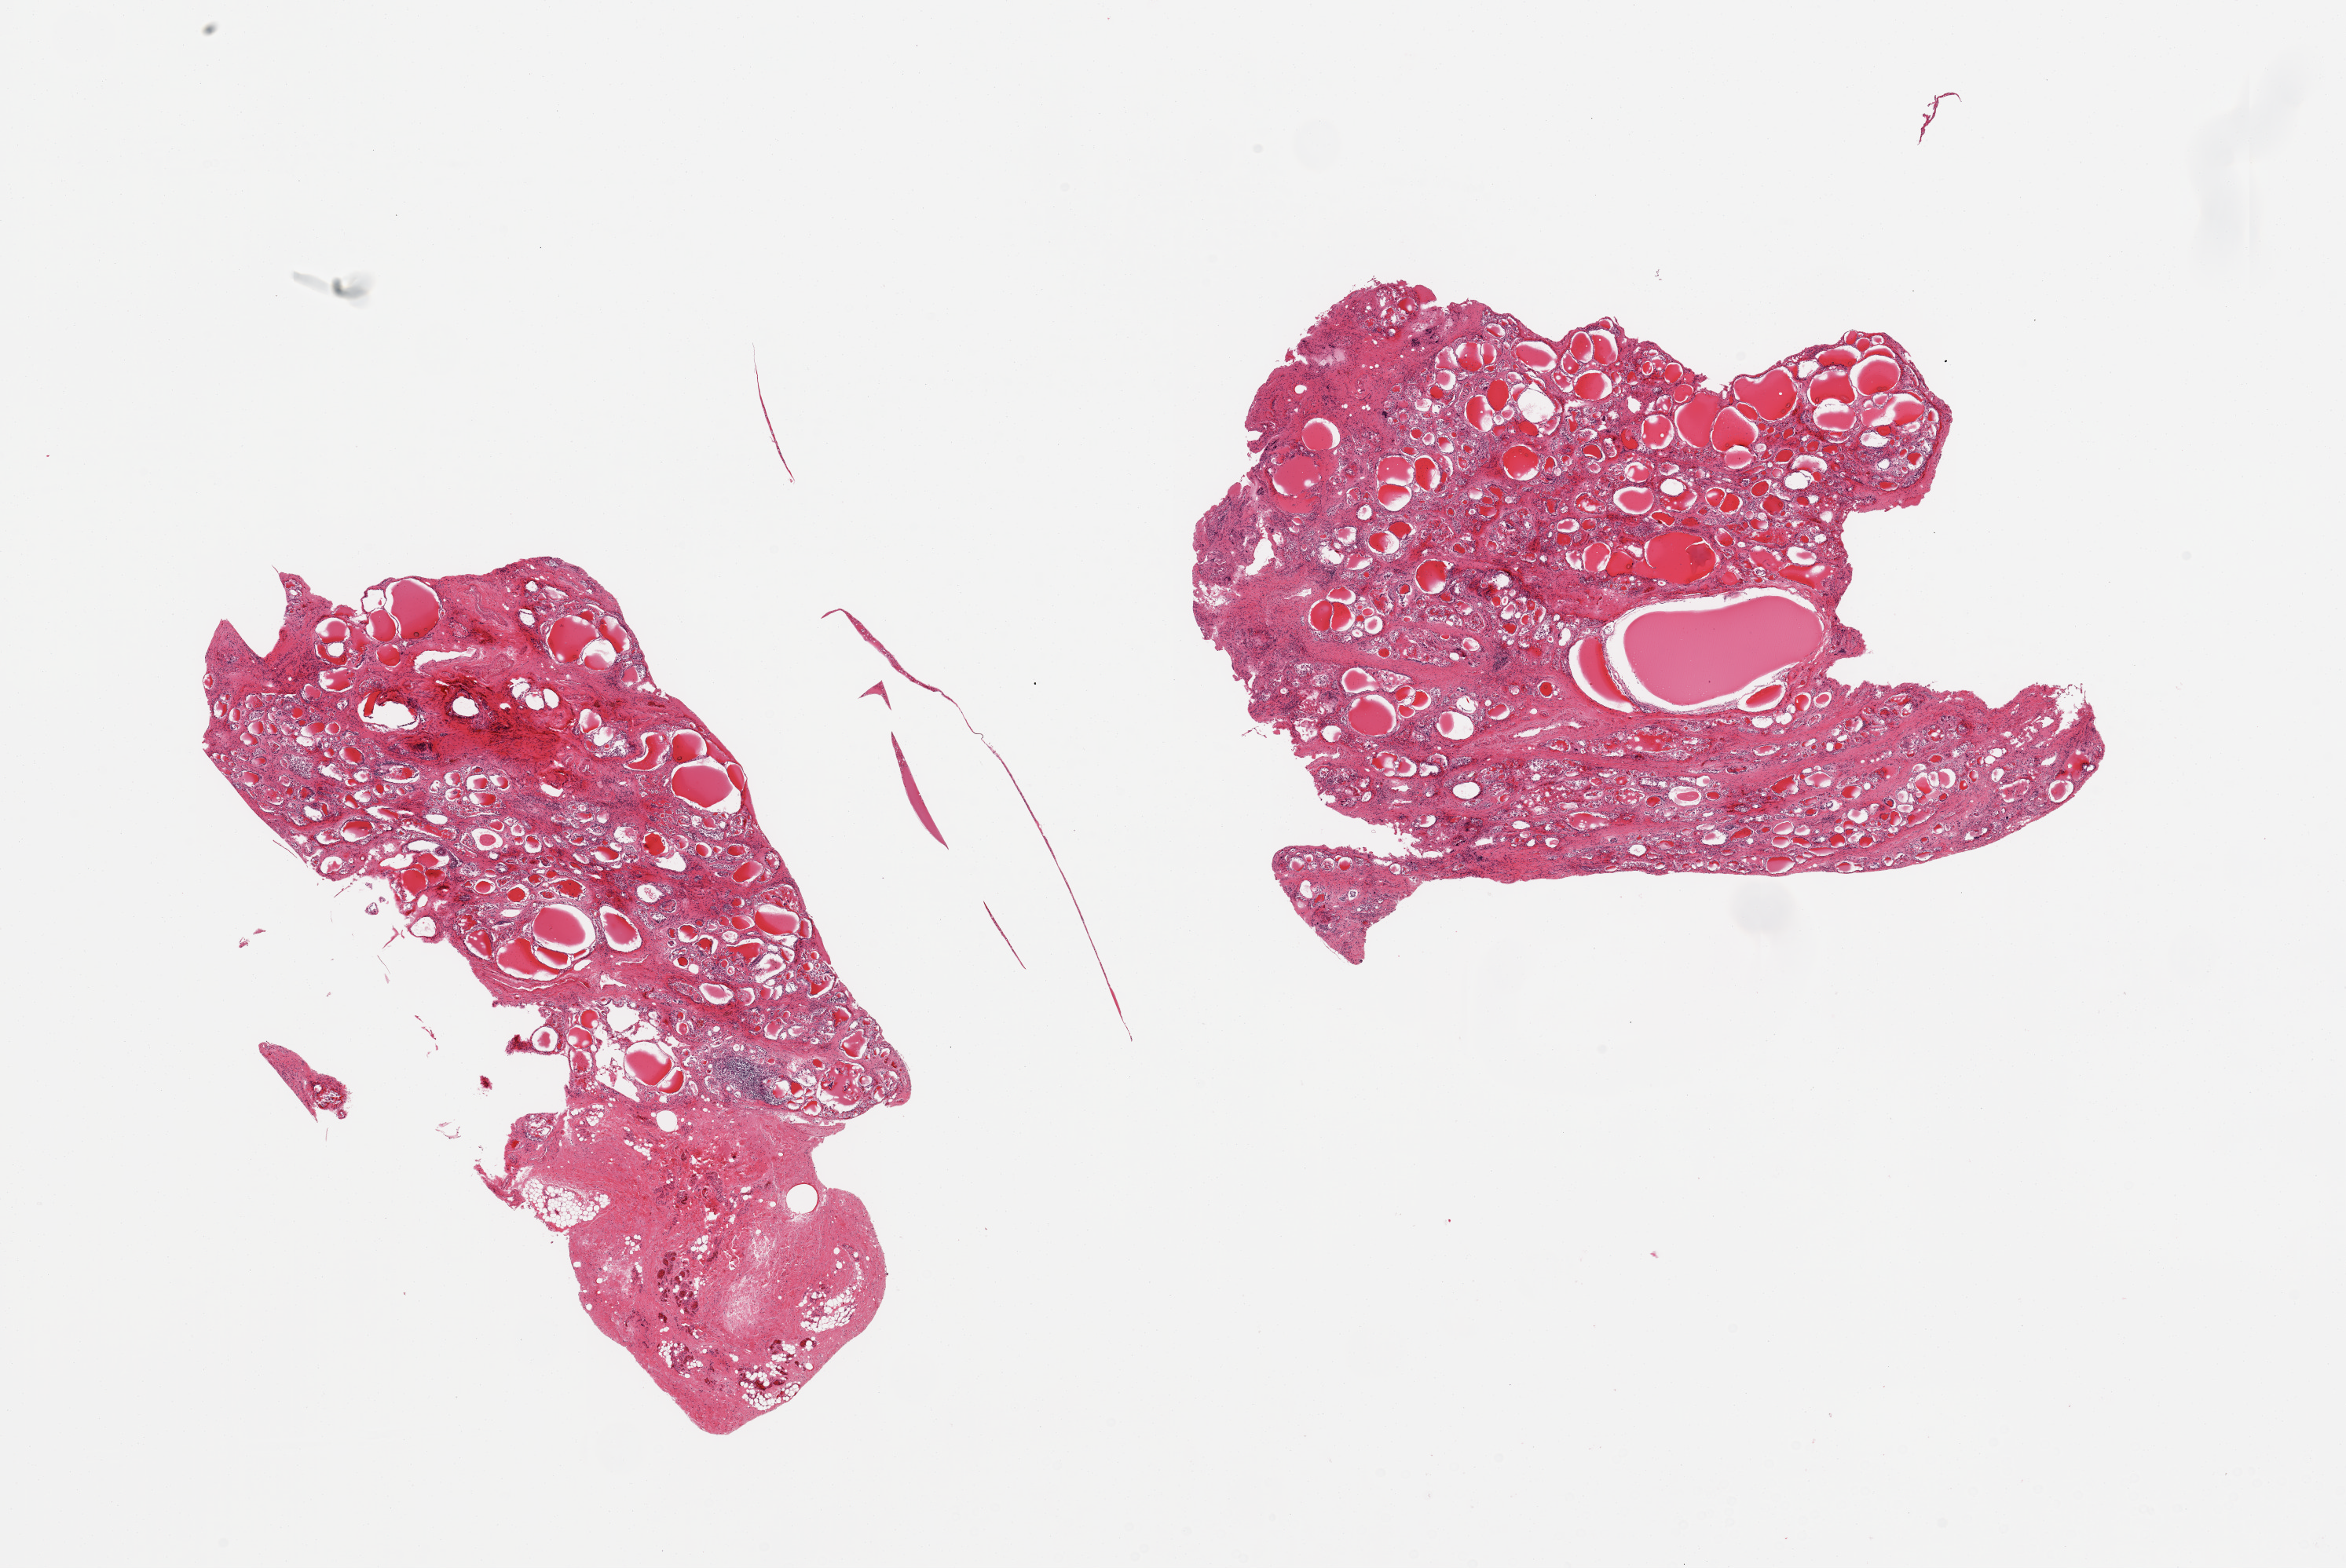
Haematoxylin and eosin whole-slide image — a low-resolution overview of the entire scanned area, about 23.6 x 15.8 mm; PAXgene-fixed paraffin-embedded (PFPE) section; target tissue: thyroid; donor tissue sample. Donor sex: male.
* reviewer comment on this tissue sample: 2 pieces; nodular goiter with regressive changes, patchy lymphocytic infiltrate; one of two pieces consists of 30% fibrovasular and adipose tissue